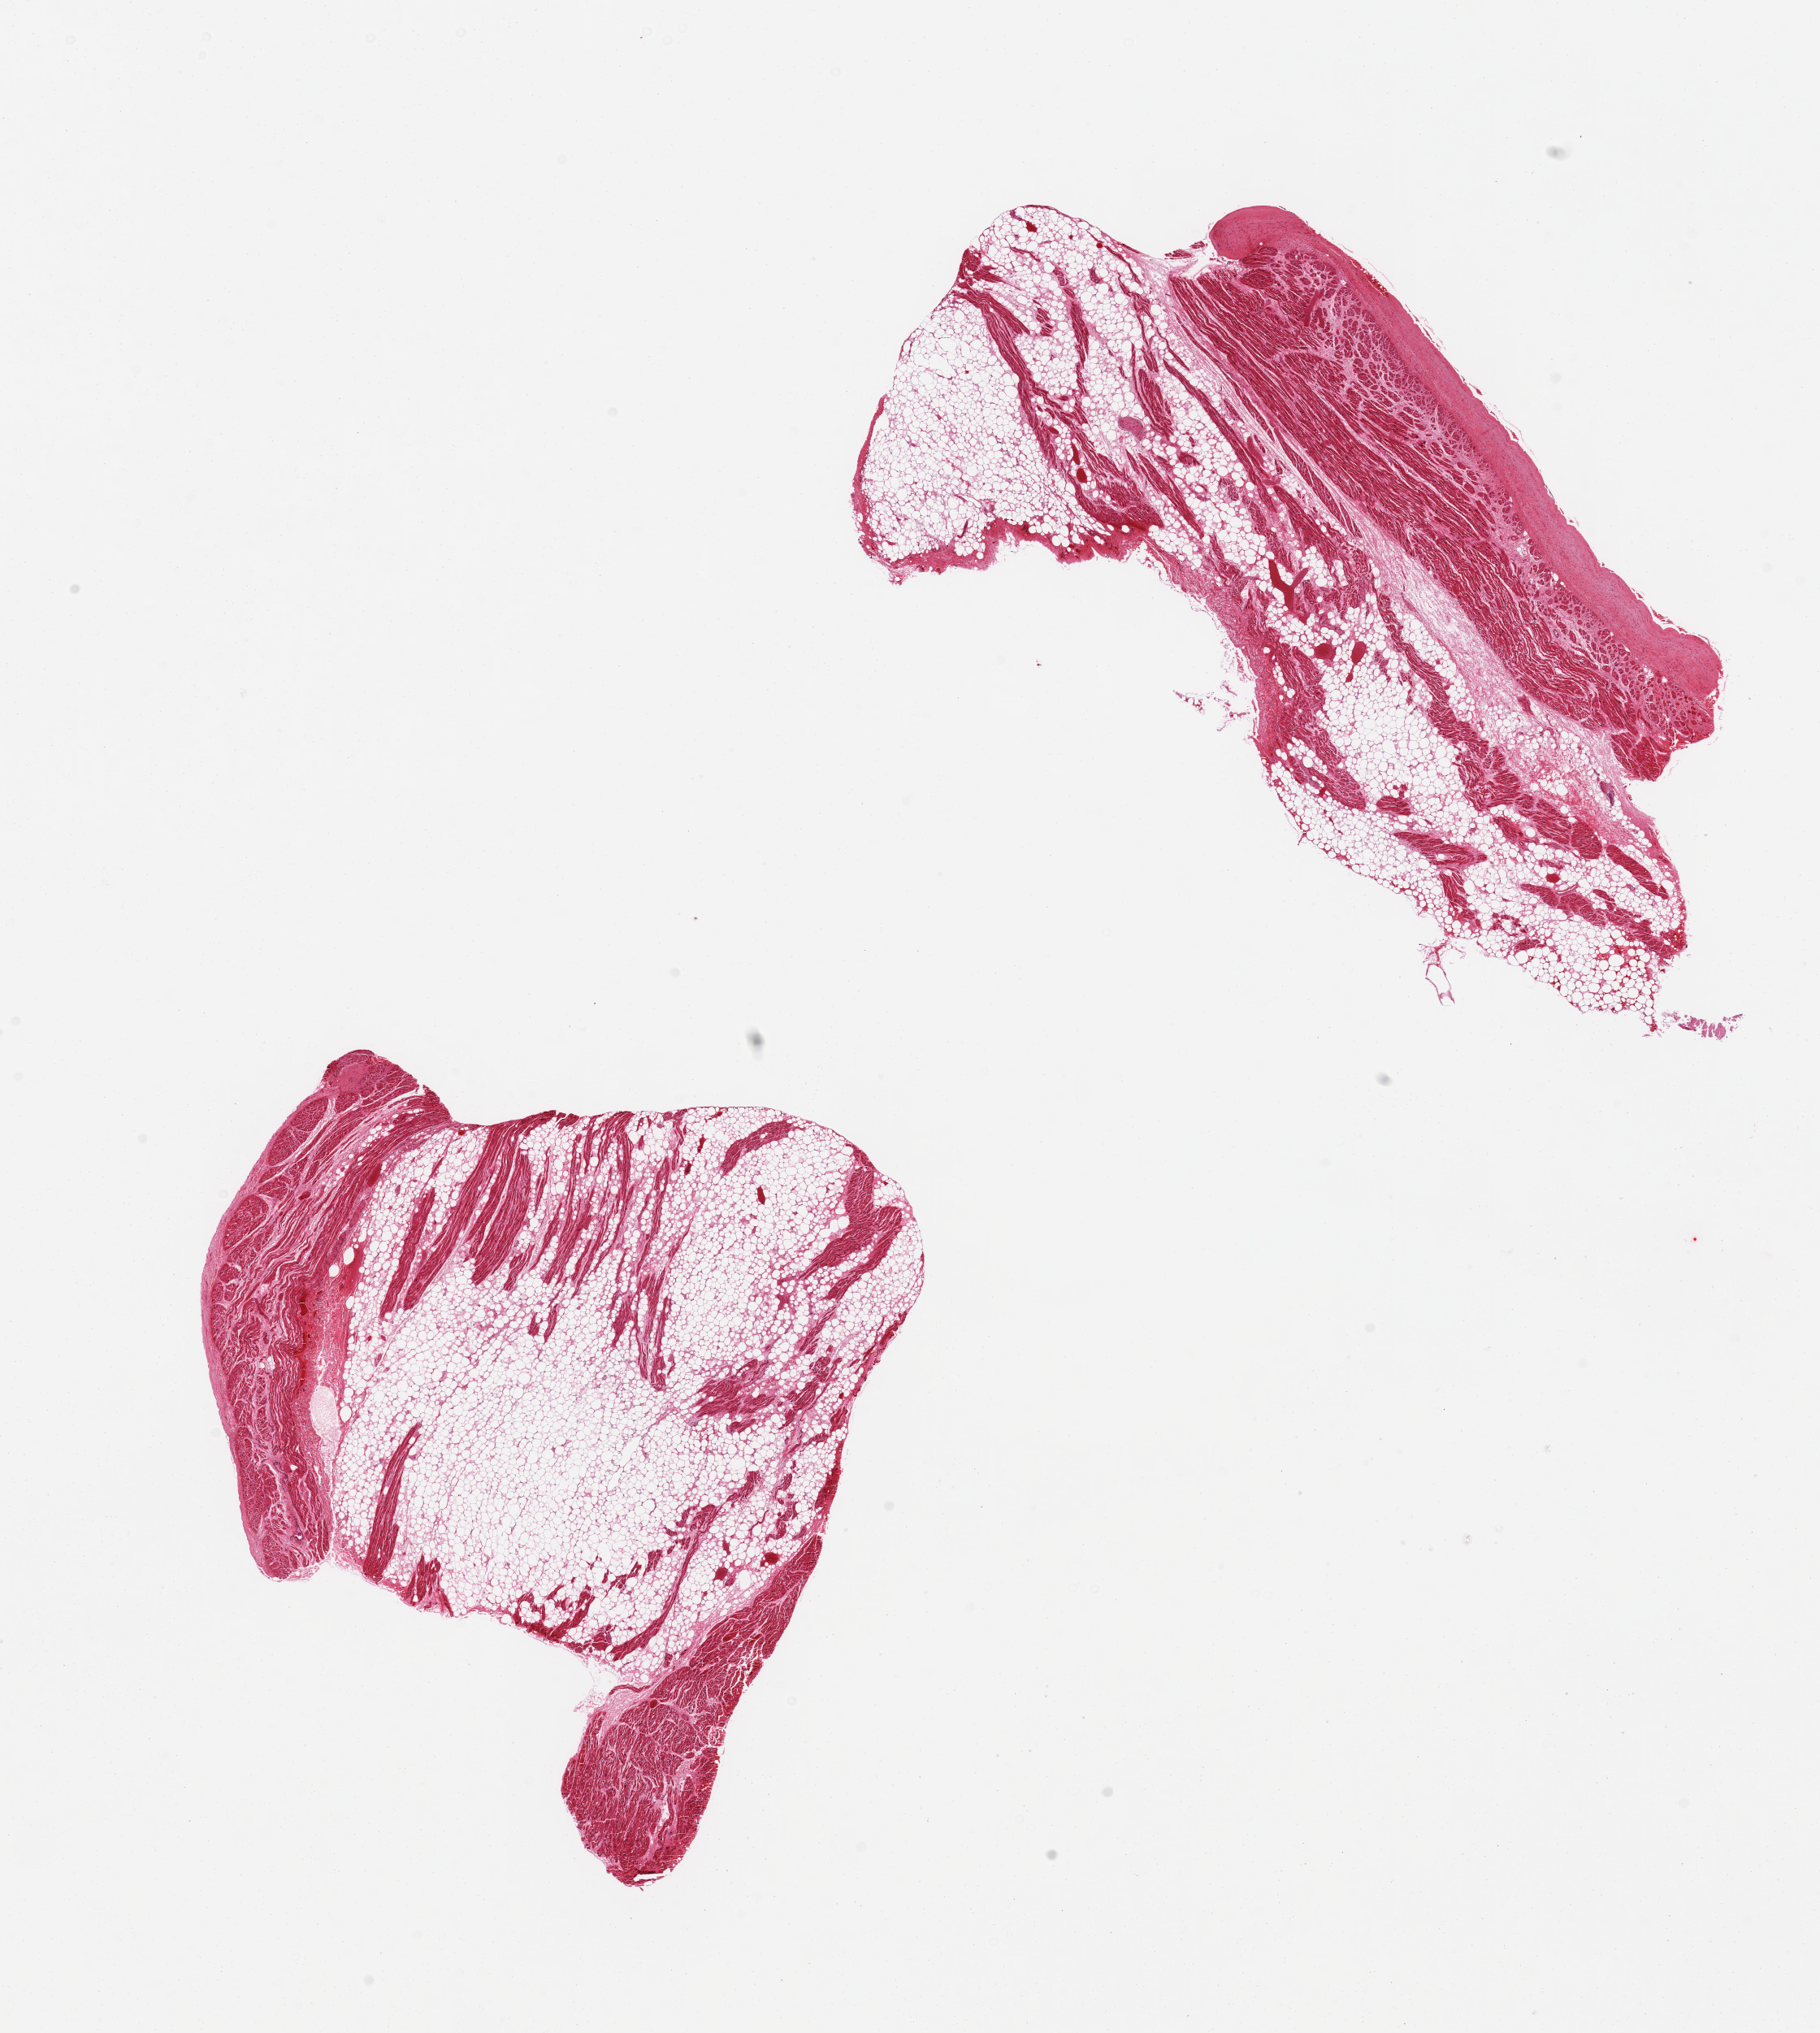
Digitized haematoxylin and eosin-stained section, brightfield, low-resolution overview of the scanned area, about 17.7 x 19.8 mm (from a 20x scan). PAXgene-fixed paraffin-embedded (PFPE) section. Sampled site (target tissue): auricular appendage. Tissue donor sample.
Review note (as recorded): 2 pieces, each is 50-70% fat.